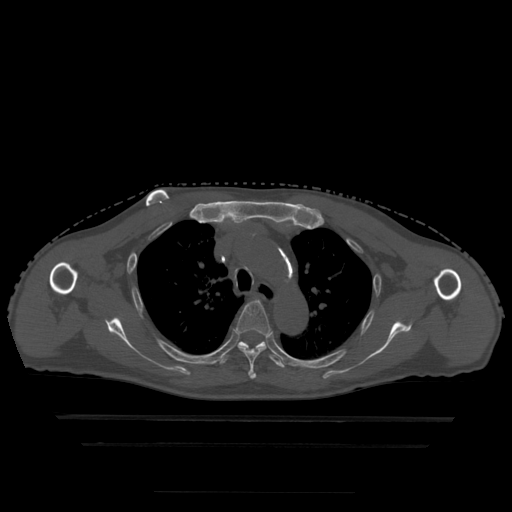
CT including the spine, one axial slice. Slice 349 of 522 in the series (ordered by position). Bone window (W 1800 / L 400 HU). 1.25 mm slice thickness. 512 × 512 image matrix. Patient age 68 years. From the clinical record (not read from this slice): primary cancer: urothelial.
Structures marked on this image (semi-automatically segmented with operator editing):
- T4 vertebra: bounding box [x1, y1, x2, y2] px = [235, 301, 272, 379]
- T5 vertebra: [219, 341, 285, 369]